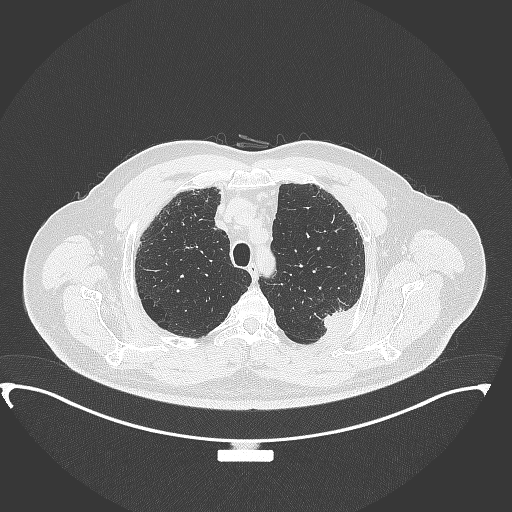
Chest CT, one axial slice. Position 291 of 350 along the scan axis. Reconstruction kernel B70f. 120 kVp. Lung window (W 1500 / L -600 HU). 512 × 512 image matrix, field of view 459 × 459 mm. Patient: male, 64 years. From the clinical record (not read from this slice): clinical TNM (as recorded): T1c N1 M1.
Outlined on this slice (rectangle marked by the reading radiologist):
- lung tumour (recorded histology: adenocarcinoma): box from (x=321, y=303) to (x=354, y=331) px